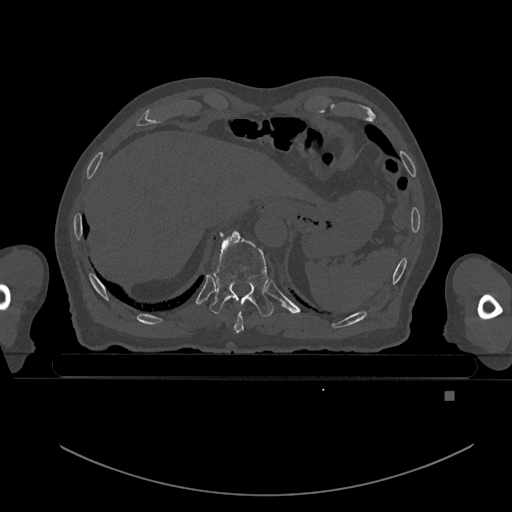
CT including the spine, one axial slice. Slice 102 of 969 in the series (ordered by position). Bone window (W 1800 / L 400 HU). 512 × 512 image matrix. Patient: male, 82 years. Case-level facts recorded for this patient, not image findings: primary cancer: prostate; vertebrae with lytic lesions (as recorded): T11, T9, T8, T2.
Annotated regions visible in this slice (semi-automatically segmented with operator editing):
- T10 vertebra: bounding box (x1, y1, x2, y2) in pixels: (210, 230, 274, 317)
- T9 vertebra: (234, 311, 244, 333)